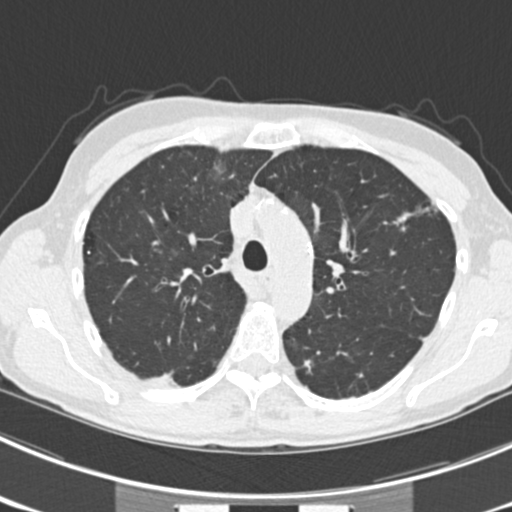
Low-dose screening chest CT, one axial slice. Slice 163 of 225 in the series (ordered by position). 120 kVp. Lung window (W 1500 / L -600 HU). 2 mm slice thickness. 512 × 512 image matrix, field of view 302 × 302 mm.
Structures marked on this image (expert manual segmentation):
- lesion 2 (tumor, lower lobe of left lung): bounding box <303,357,313,374> (left, top, right, bottom; pixels)